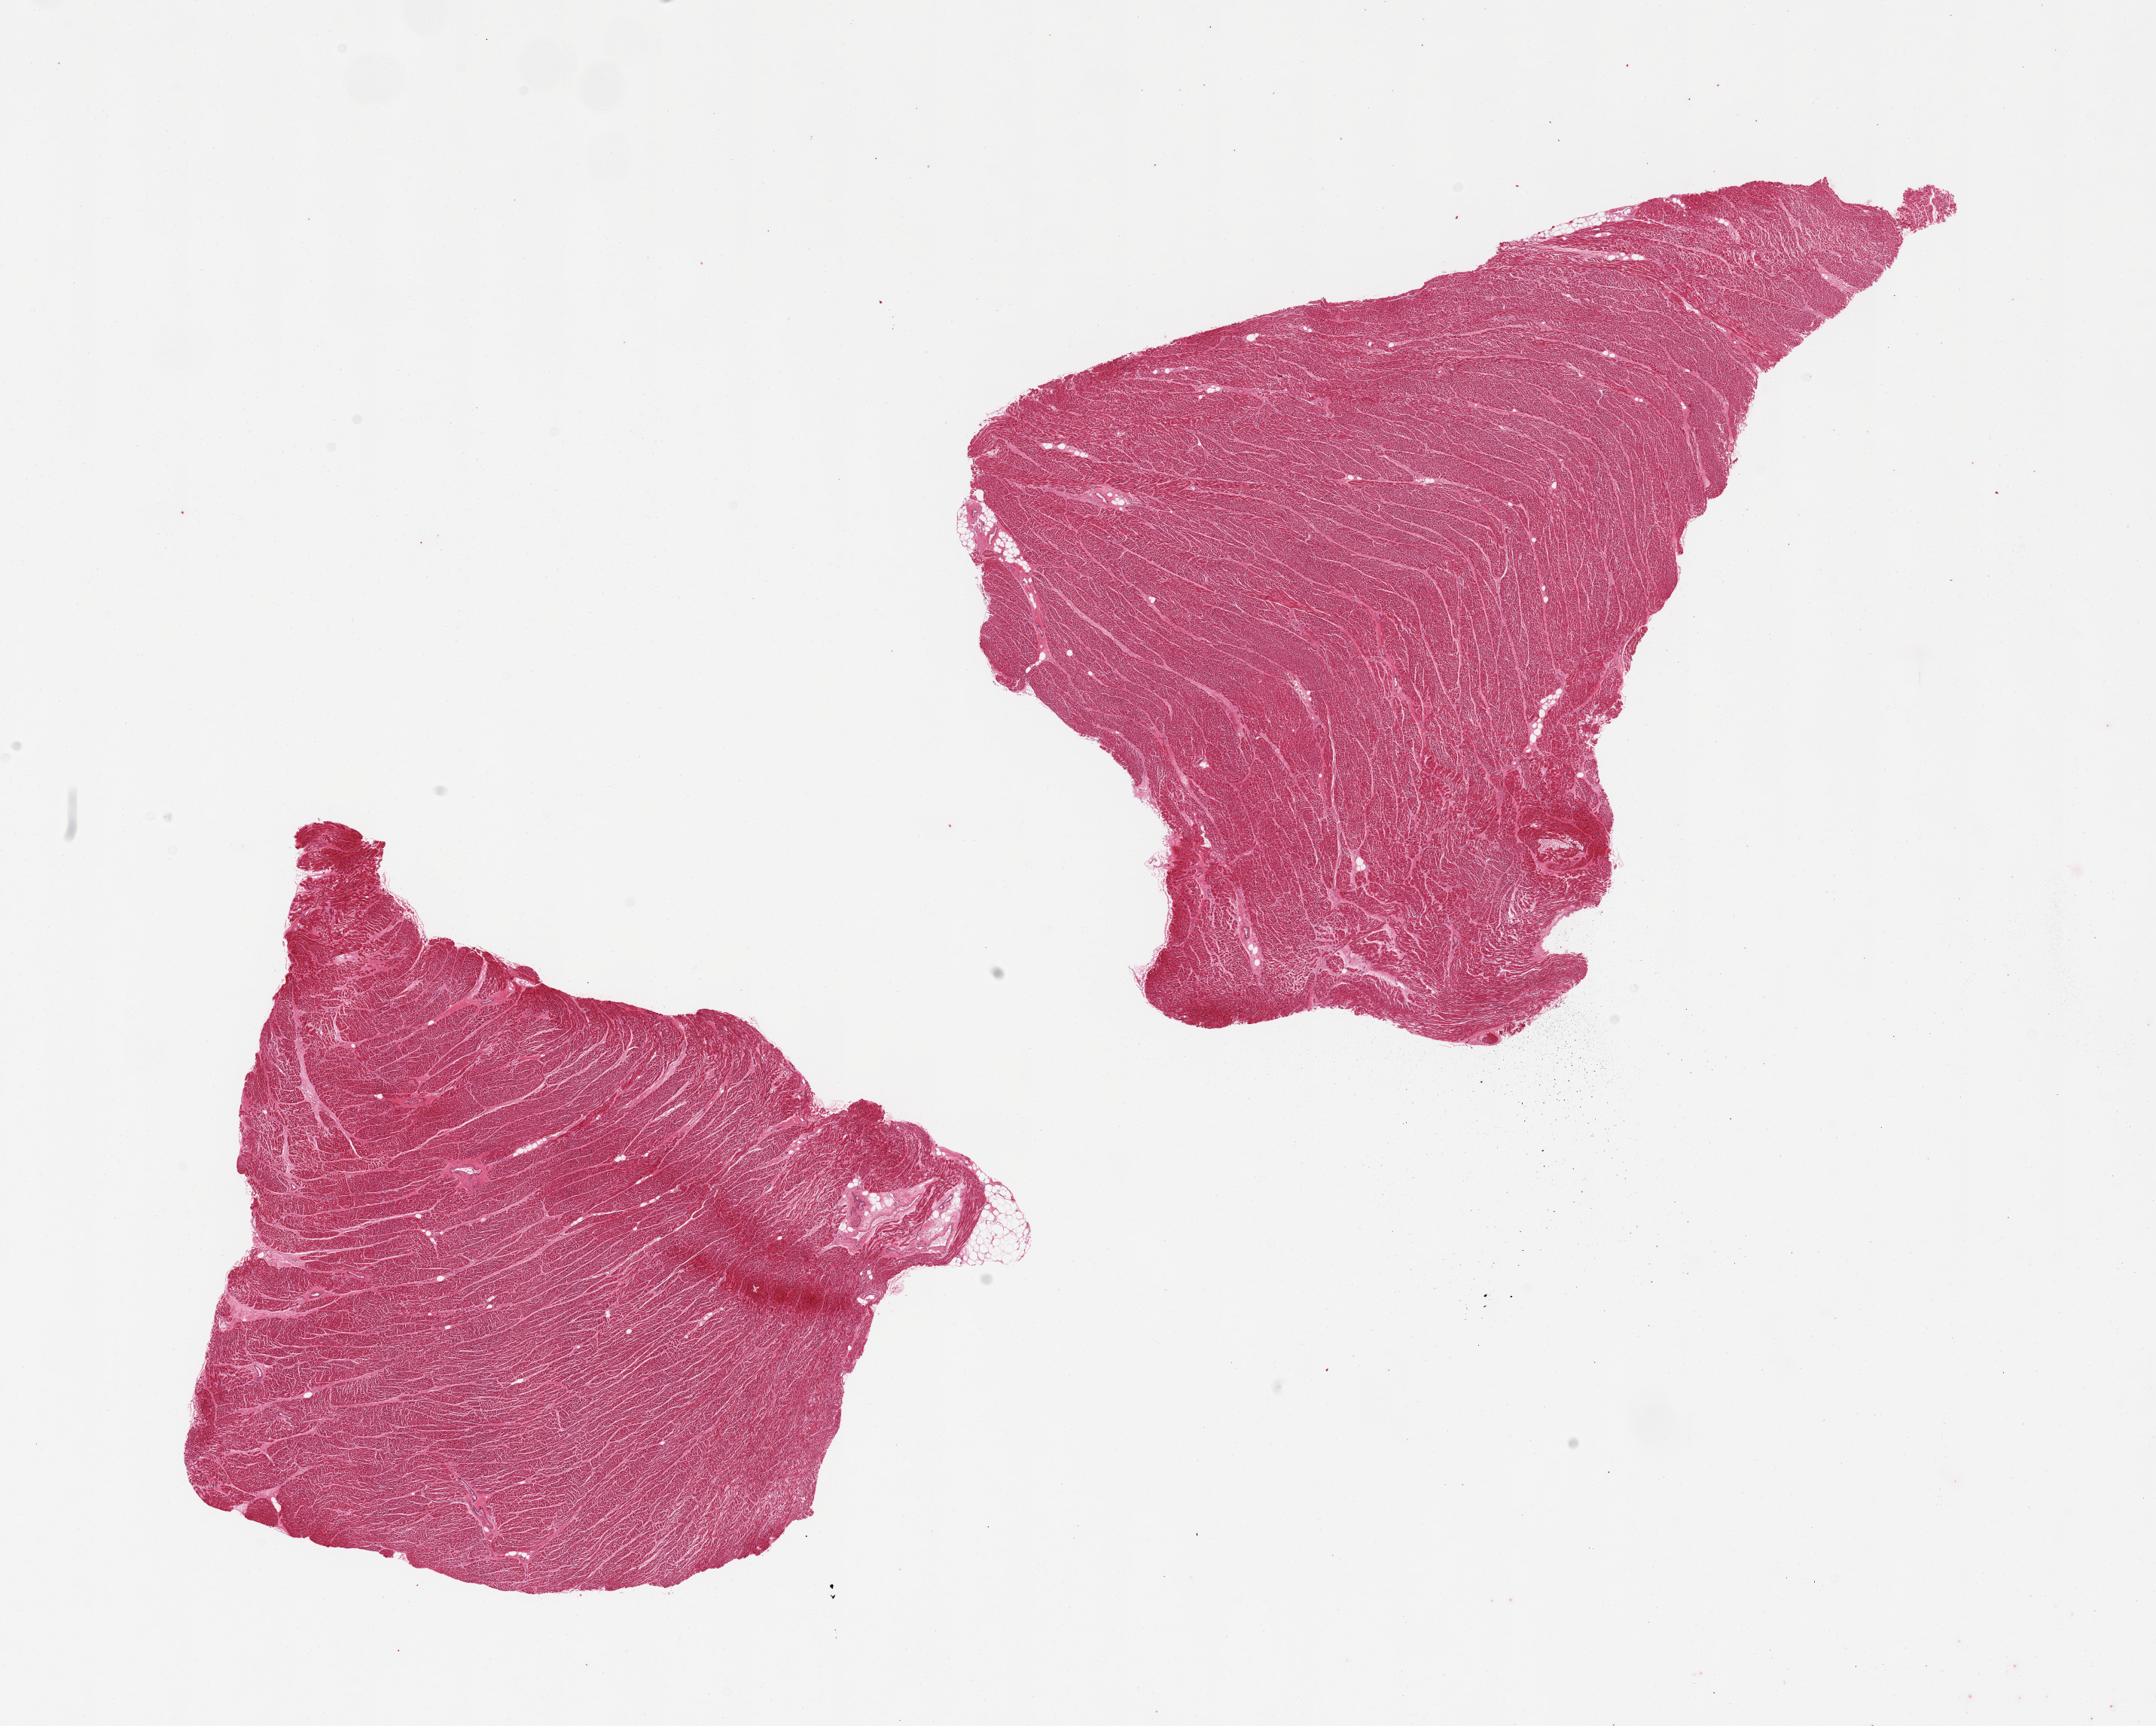
Hematoxylin and eosin (H&E) whole-slide image, shown as a low-resolution overview of the whole scanned area (about 22.6 x 18.1 mm); PAXgene-fixed, paraffin-embedded tissue; sampled site (target tissue): heart; donor tissue sample.
- reviewer comment on this tissue sample: 2 pieces